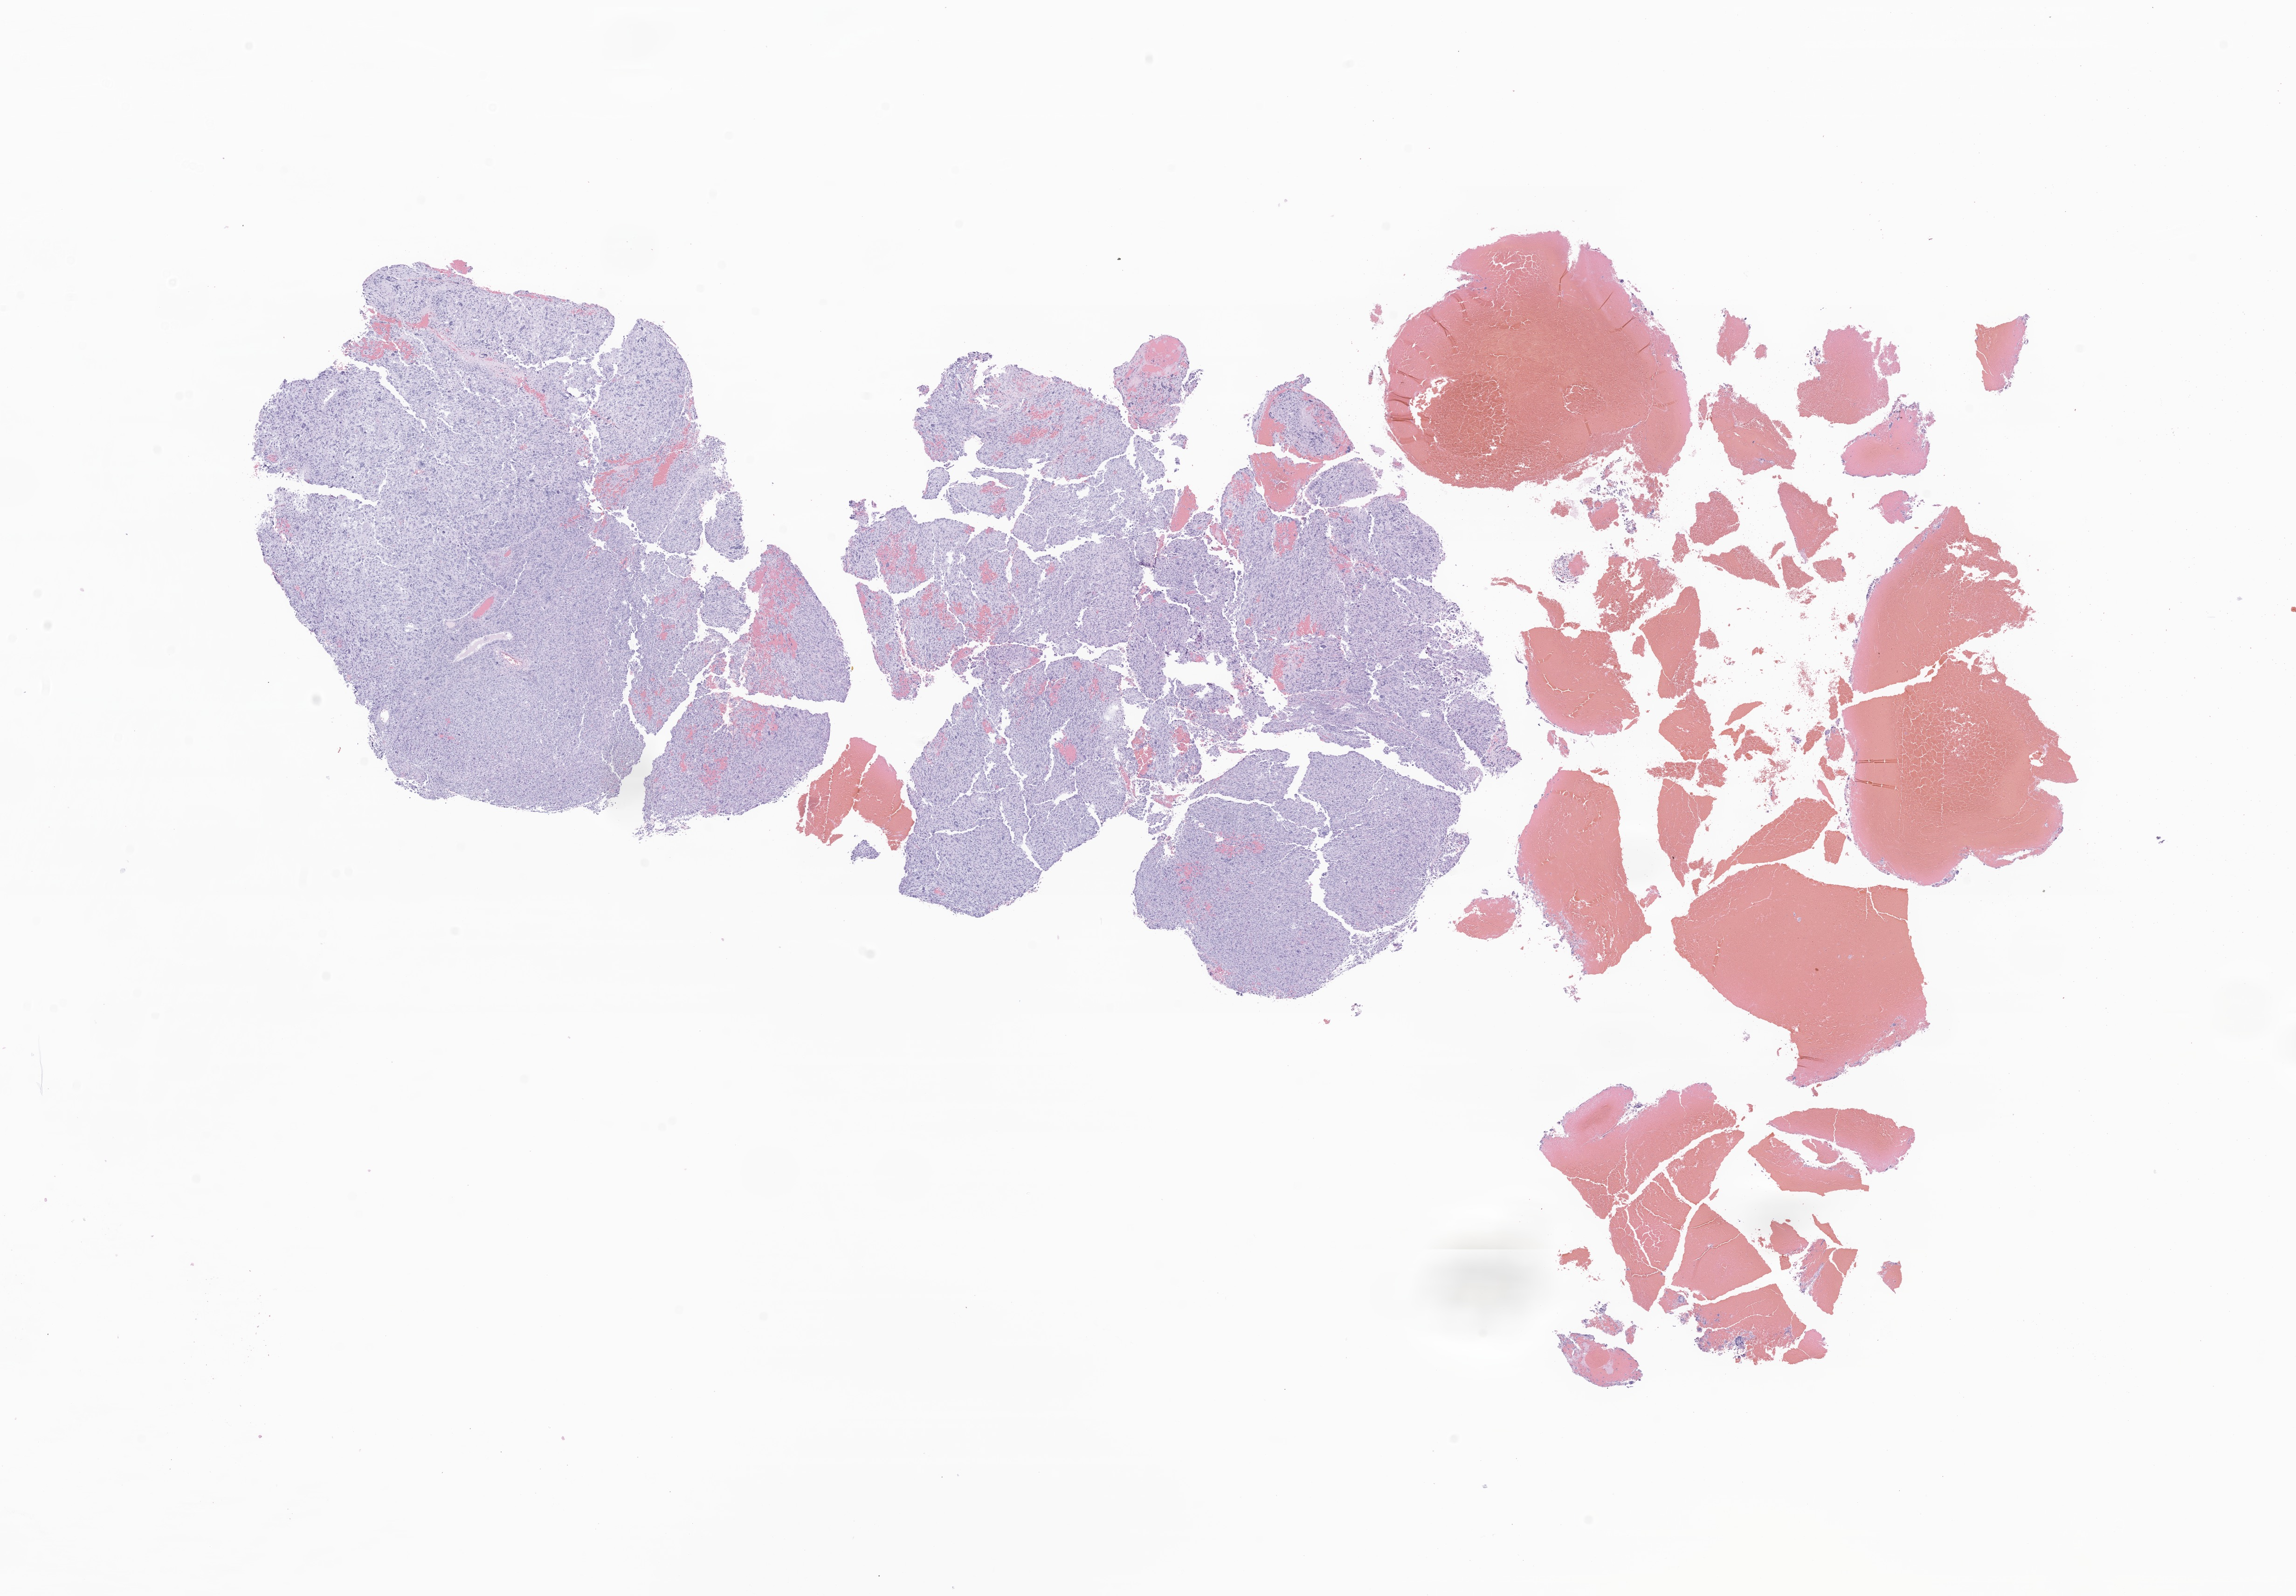
Digitized hematoxylin and eosin (H&E)-stained section of tumor tissue from the brain — whole scanned area (about 20.8 x 14.4 mm) shown as a low-resolution overview; formalin-fixed, paraffin-embedded (FFPE) tissue. Patient female; age 94 months (7 years 10 months).
Recorded diagnosis: Neoplasm, uncertain whether benign or malignant.